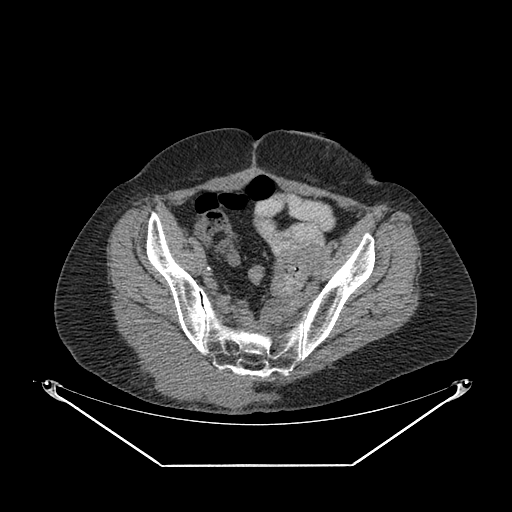
CT of an extremity soft-tissue mass (from a PET/CT study), one axial slice. Position 69 of 267 along the scan axis. Reconstruction kernel SOFT. 140 kVp. Soft-tissue window (W 400 / L 40 HU). 3.75 mm slice thickness. 512 × 512 image matrix, field of view 500 × 500 mm. Female patient. Case-level facts recorded for this patient, not image findings: histological type: spindle cell suggestive of myxofibrosarcoma; grade: intermediate; site of the primary tumour: right buttock.
Outlined on this slice (expert contour drawn on MRI and transferred to this co-registered scan by the dataset authors):
- gross tumour volume (mass): bounding box (x1, y1, x2, y2) in pixels: (130, 336, 250, 407)